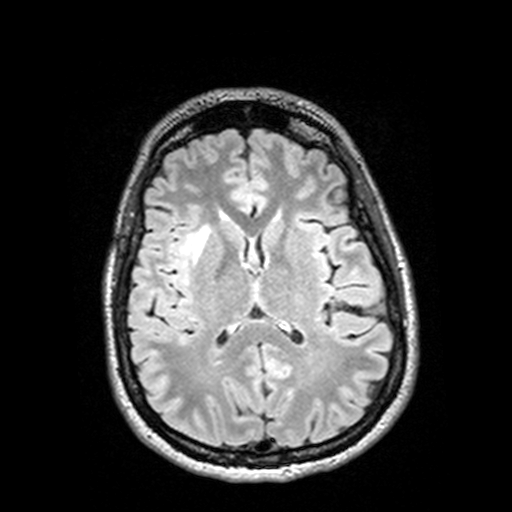
Brain MRI from a brain-tumour surgery series, one axial slice; slice 63 of 144 in the series (ordered by position); T2 FLAIR; 1 mm slice thickness; 512 × 512 image matrix, field of view 250 × 250 mm. From the clinical record (not read from this slice): histopathology: Astrocytoma; WHO grade: 3; IDH mutation: yes; tumour location: Right Insular Temporal.
Outlined on this slice (outlined manually by an expert reader):
- tumour: bounding box [x1, y1, x2, y2] px = [192, 226, 220, 264]